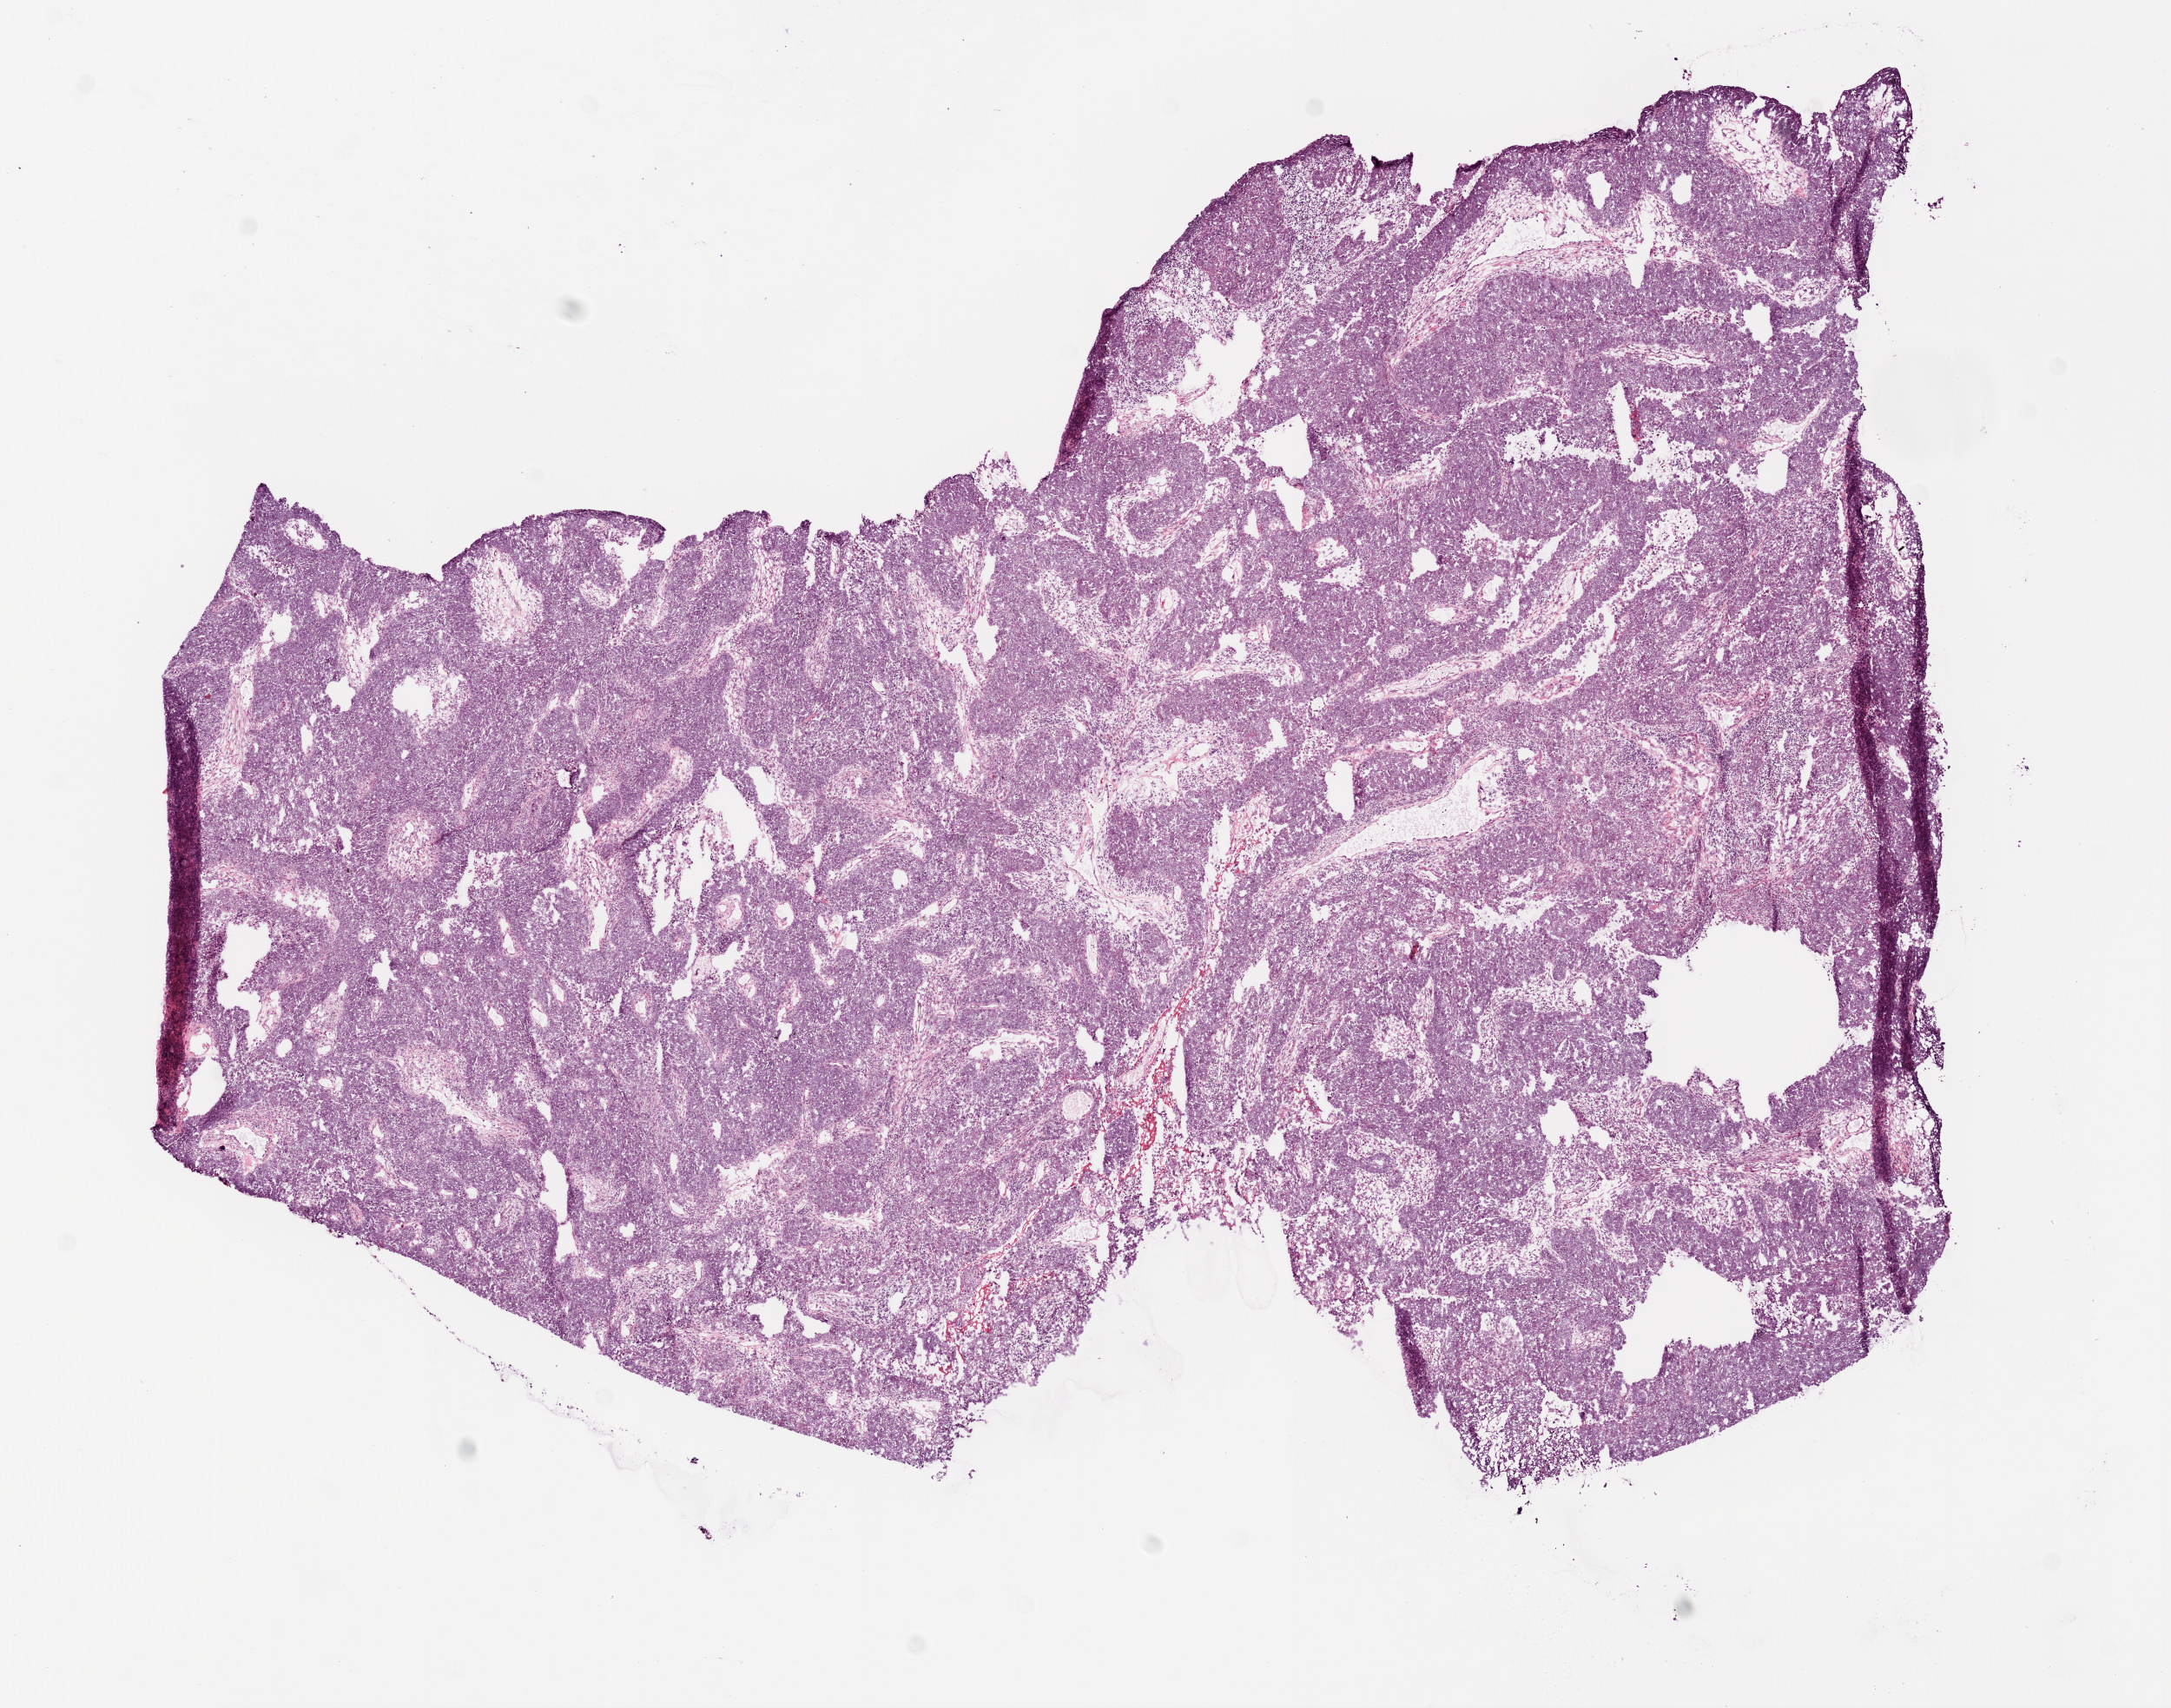
H&E whole-slide image — low-resolution overview of the scanned area, about 10.0 x 7.9 mm. Frozen section from the bottom of the tissue portion. Sample: primary tumour, ovary. Female, age 61 years at initial diagnosis. Histologic grade: G2 (moderately differentiated). Composition of this section per pathologist review: tumour cells 90%, tumour nuclei 90%, normal cells 0%, stromal cells 7%, necrosis 3%.
• pathologic diagnosis: Serous cystadenocarcinoma, NOS
• laterality: bilateral
• FIGO stage: IIC